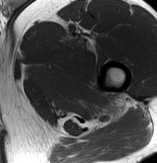
MRI of an extremity soft-tissue mass, one axial slice. Position 67 of 70 along the scan axis. MR volume resampled by the dataset authors to the PET/CT grid (not the native acquisition matrix). 157 × 163 image matrix. Male patient. From the clinical record (not read from this slice): histological type: extraskeletal osteosarcoma; grade: high; site of the primary tumour: left adductur.
Outlined on this slice (expert contour drawn on MRI and transferred to this co-registered scan by the dataset authors):
- gross tumour volume (mass): bounding box (x1, y1, x2, y2) in pixels: (26, 24, 128, 123)